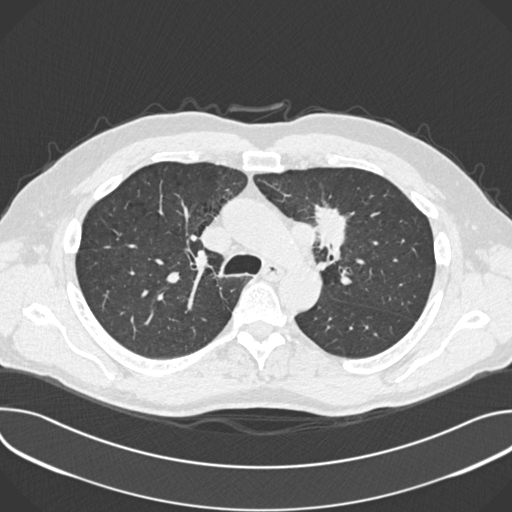
Low-dose screening chest CT, one axial slice; lung window (W 1500 / L -600 HU); 512 × 512 image matrix.
Annotated regions visible in this slice (outlined manually by an expert reader):
- lesion 1 (tumor, upper lobe of left lung): bounding box <315,207,347,248> (left, top, right, bottom; pixels)